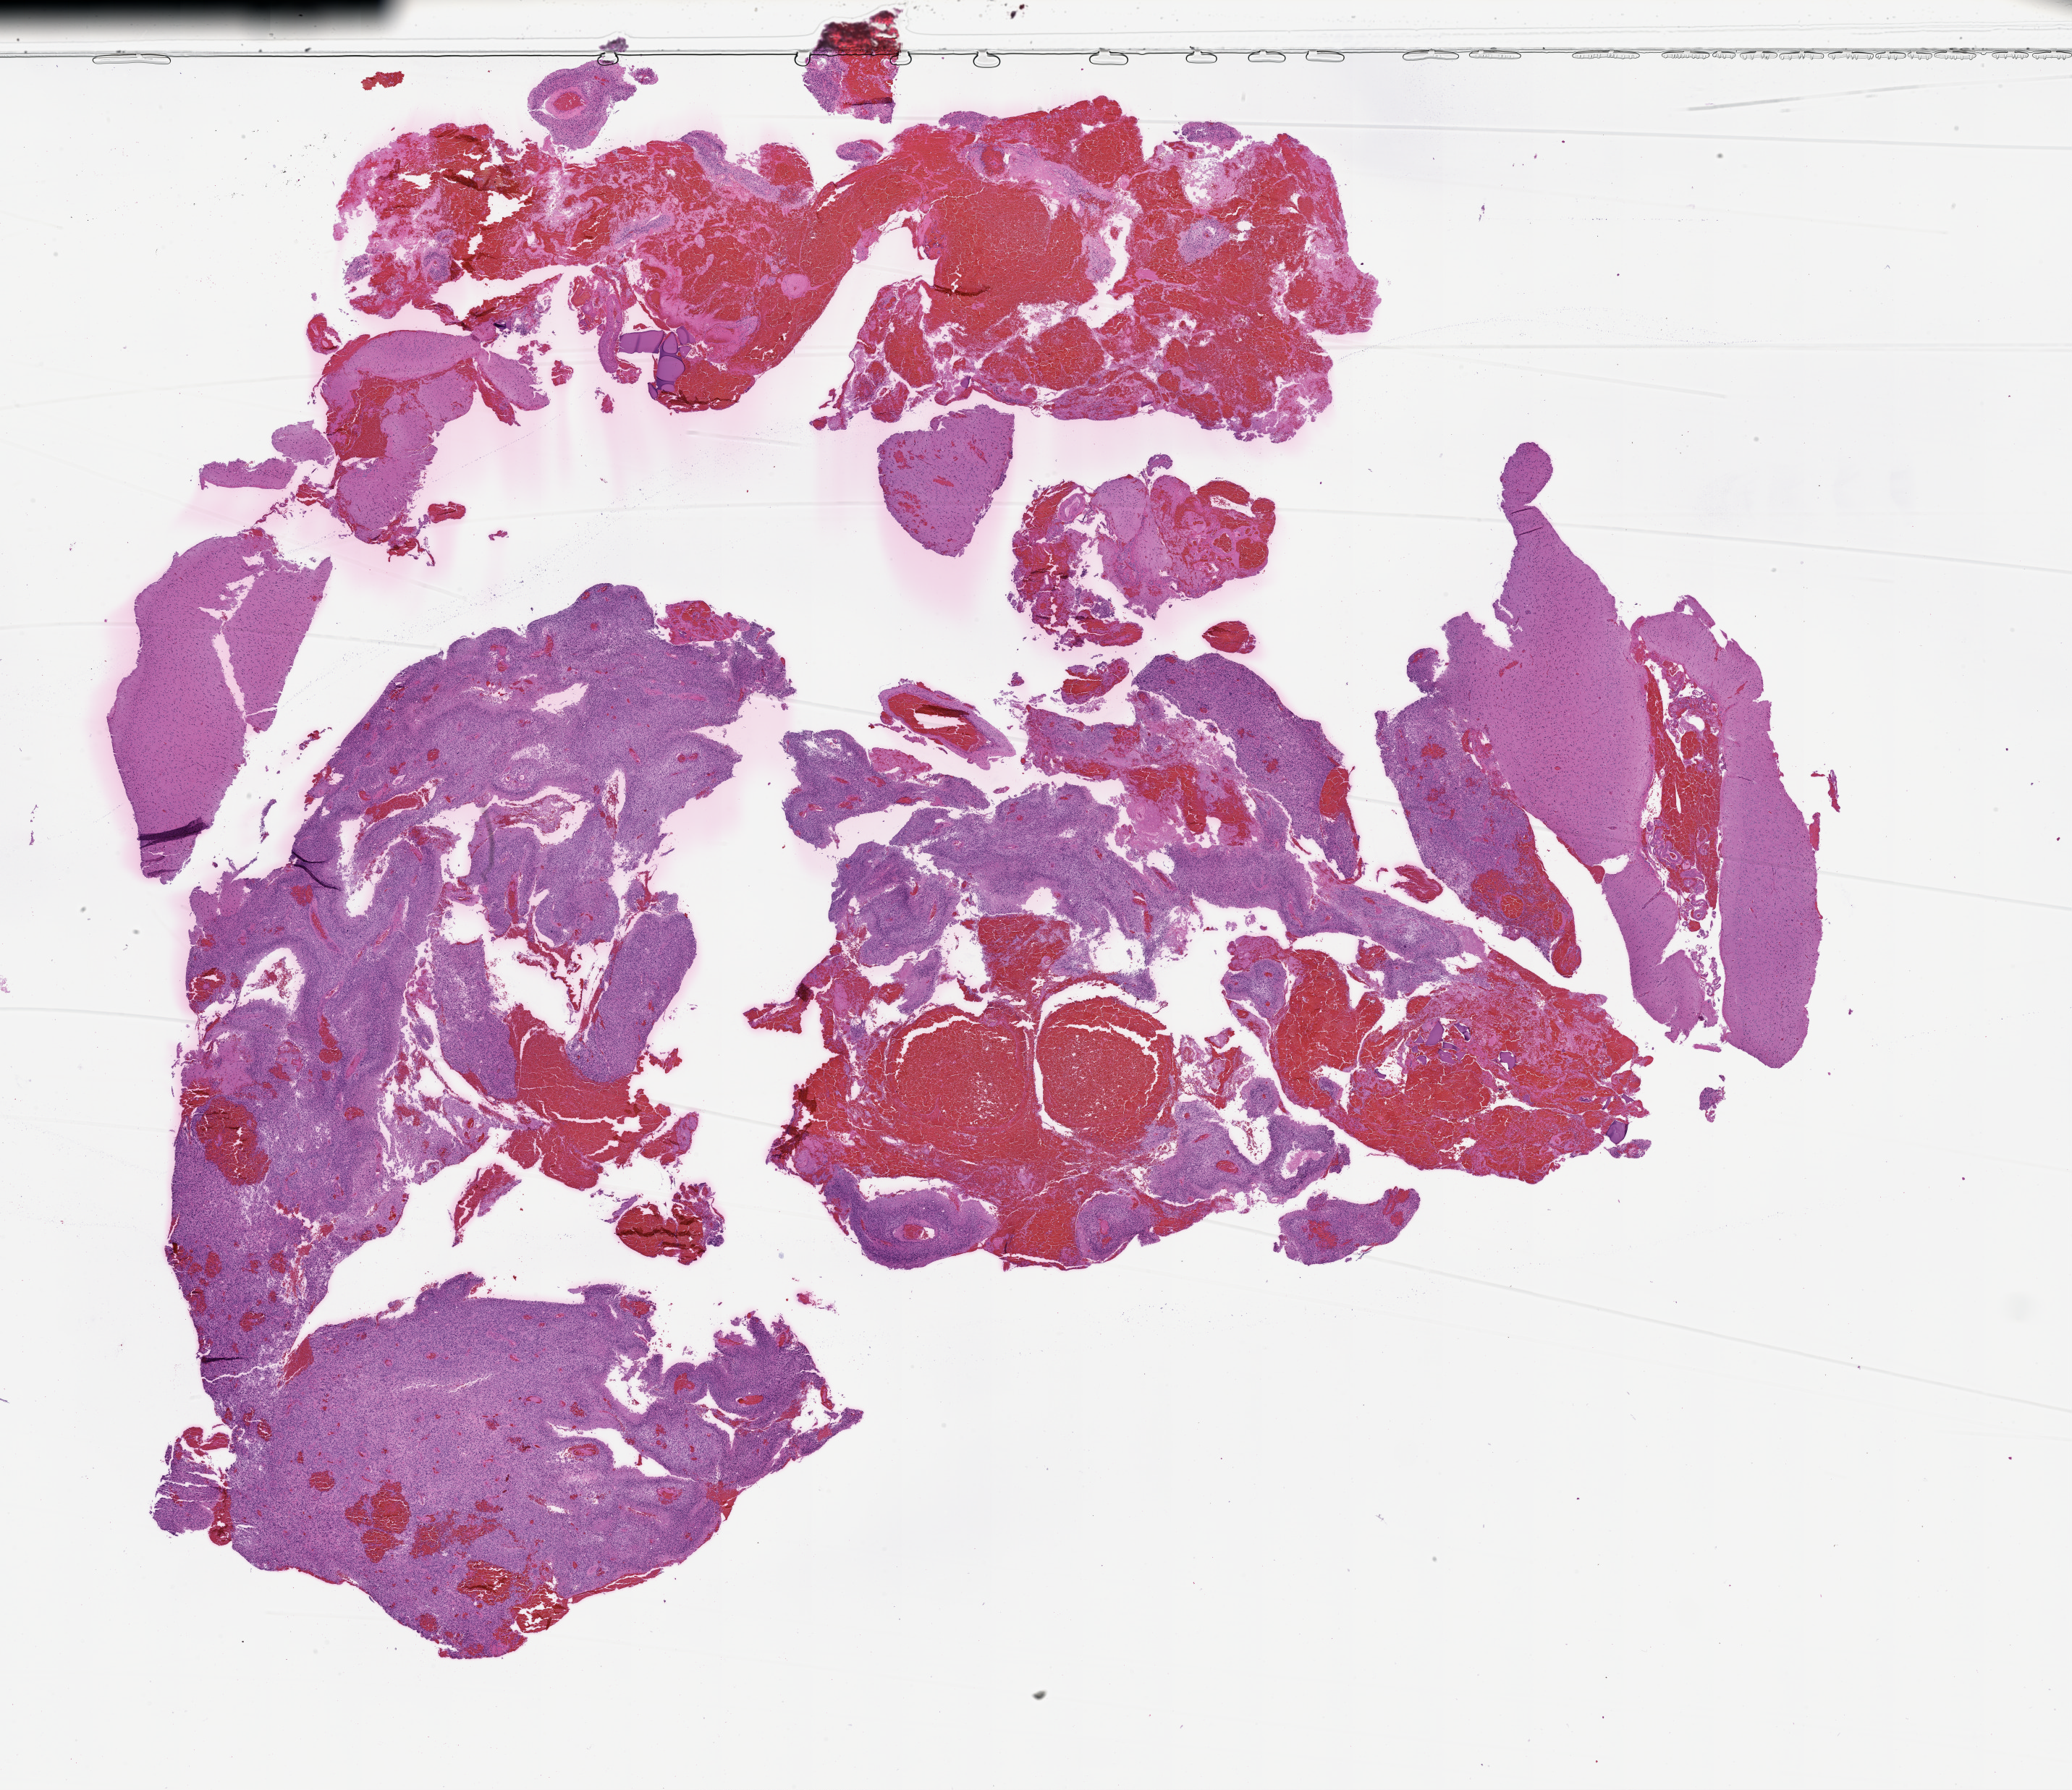
H&E-stained whole-slide image, whole scanned area (about 23.1 x 19.9 mm) shown as a low-resolution overview, tumour tissue sample, sampled site: brain. 69-year-old female patient. Composition of this section per pathologist review: tumour nuclei 70%, necrosis 10%.
Primary tumour site (as recorded): parietal lobe. Diagnosis: Glioblastoma.